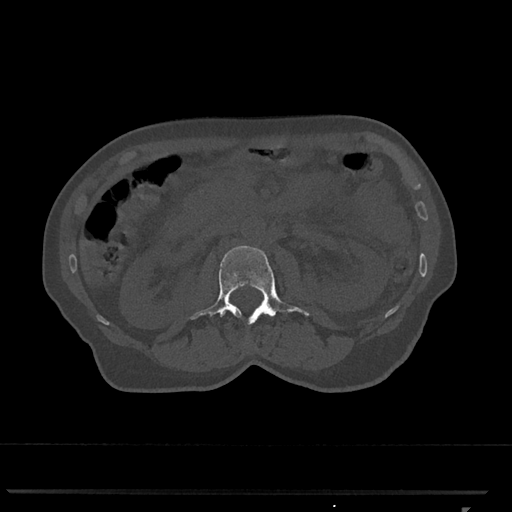
CT including the spine, one axial slice. Position 344 of 793 along the scan axis. Bone window (W 1800 / L 400 HU). 0.5 mm slice thickness. 512 × 512 image matrix, field of view 380 × 380 mm. Patient: female, 62 years. Case-level facts recorded for this patient, not image findings: primary cancer: renal.
Outlined on this slice (semi-automatic segmentation, software-assisted and operator-edited):
- L2 vertebra: bounding box <190,245,309,325> (left, top, right, bottom; pixels)